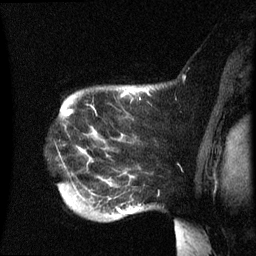
Breast MRI (dynamic contrast-enhanced), one sagittal slice. Slice 53 of 60 in the series (ordered by position). Dynamic contrast-enhanced series, image 2 of 3 at this slice position (ordered by acquisition). 1.5 T. TE 4.2 ms, TR 8.4 ms. 2.5 mm slice thickness. 256 × 256 image matrix, field of view 220 × 220 mm. Patient: female, 49 years.
Structures marked on this image (semi-automatic segmentation, software-assisted and operator-edited):
- analysis volume of interest (the breast-tissue region the enhancement analysis was run in; not a lesion): bounding box <60,86,185,235> (left, top, right, bottom; pixels)
- tumour enhancement mask (voxels above the 70 % enhancement threshold inside the analysis volume of interest): <67,110,123,213>